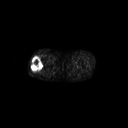
FDG PET of an extremity soft-tissue mass (from a PET/CT study), one axial slice. Position 243 of 267 along the scan axis. 128 × 128 image matrix, field of view 700 × 700 mm. Patient: male, 43 years. From the clinical record (not read from this slice): histological type: poorly differentiated synovial sarcoma; grade: high; site of the primary tumour: right buttock.
Outlined on this slice (expert contour drawn on MRI and transferred to this co-registered scan by the dataset authors):
- gross tumour volume including surrounding oedema: box from (x=31, y=58) to (x=43, y=73) px
- gross tumour volume (mass): (x=31, y=58)–(x=43, y=73)